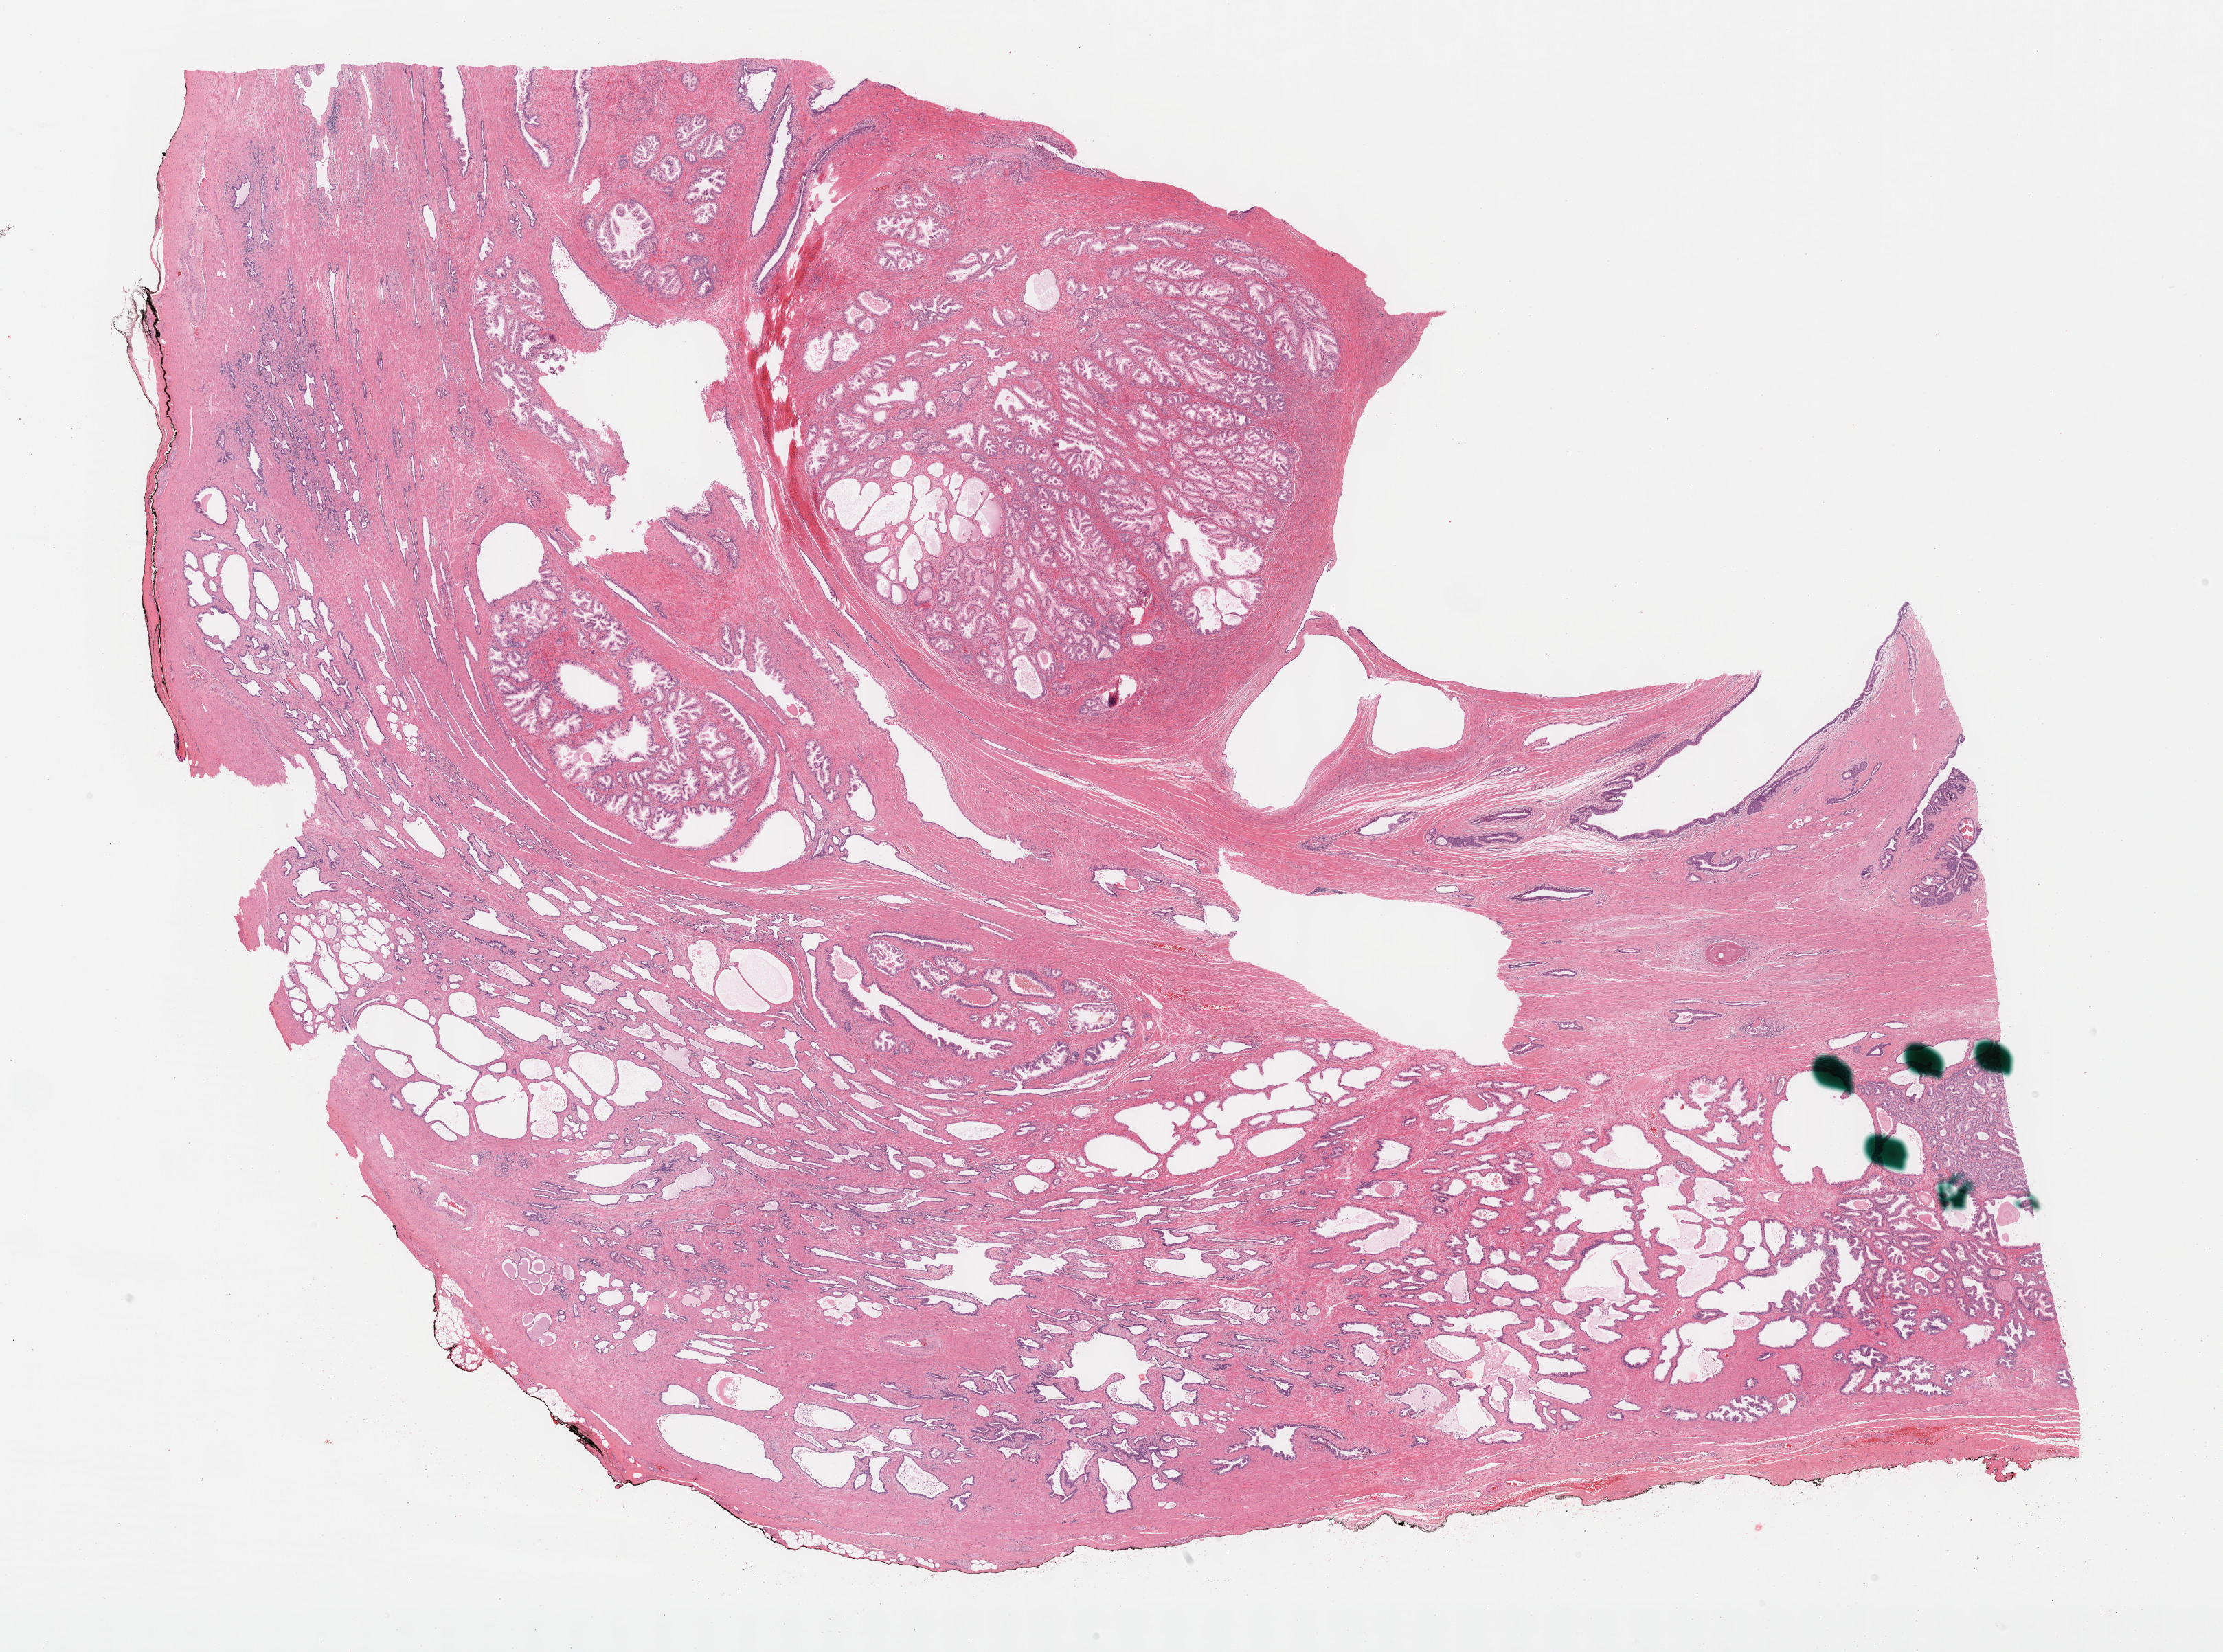
Whole-slide histology image, Hematoxylin and eosin (H&E) stained — whole scanned area (about 26.2 x 19.5 mm, slide scanned at 40x) shown as a low-resolution overview; FFPE section; prostate, primary tumour sample. Patient: male, age at initial diagnosis 61 years. Gleason score: 6 (3+3).
Histologic diagnosis: Adenocarcinoma, NOS (prostate gland). Laterality: bilateral.